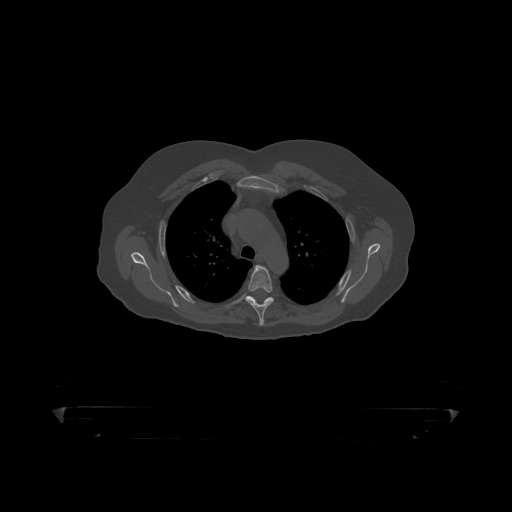
CT including the spine, one axial slice; reconstruction kernel STANDARD; 120 kVp; bone window (W 1800 / L 400 HU); 1.25 mm slice thickness; 512 × 512 image matrix, field of view 650 × 650 mm. Male patient, age 60 years. From the clinical record (not read from this slice): primary cancer: prostate.
Annotated regions visible in this slice (semi-automatically segmented with operator editing):
- T4 vertebra: box from (x=245, y=266) to (x=274, y=319) px
- T5 vertebra: (x=236, y=296)–(x=283, y=314)